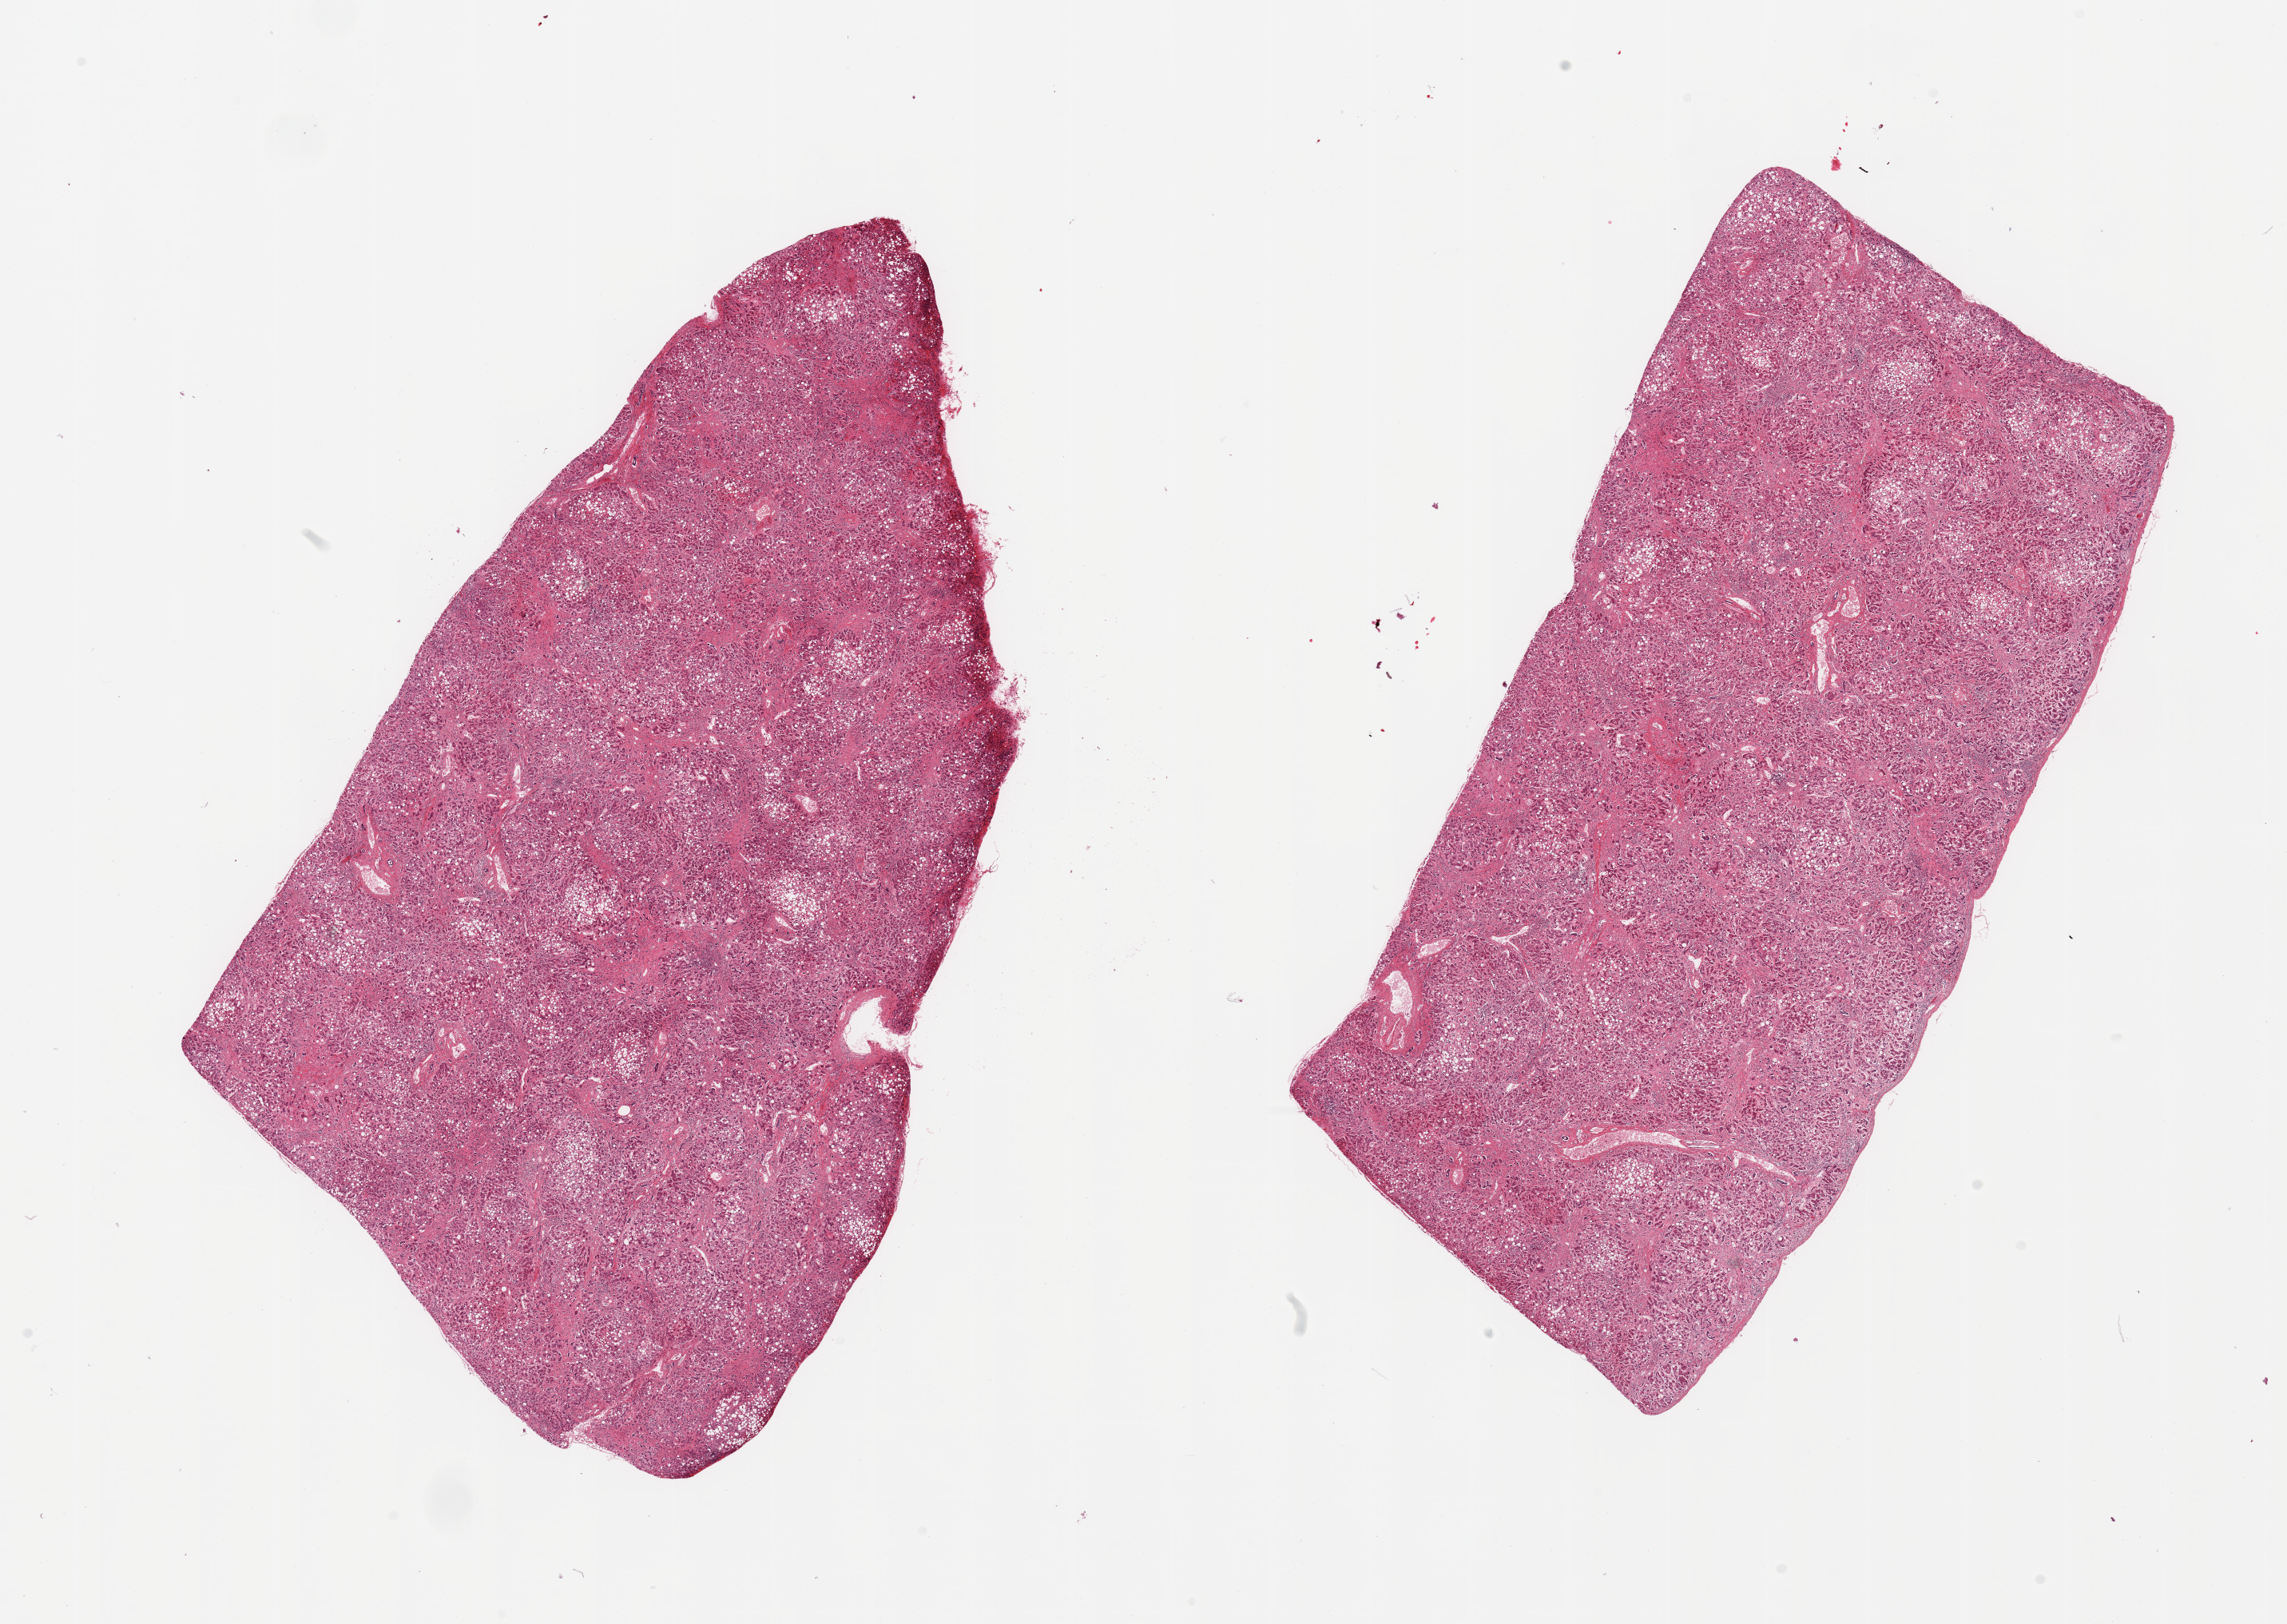
Digitized hematoxylin and eosin (H&E)-stained section, low-resolution overview of the scanned area, about 22.6 x 16.1 mm. PAXgene-fixed, paraffin-embedded tissue. Target tissue: liver. Tissue donor sample. Male donor.
Reviewer comment on this tissue sample: 2 pieces; fatty degeneration, fibrosis consistent with cirrhosis, and inflammation.